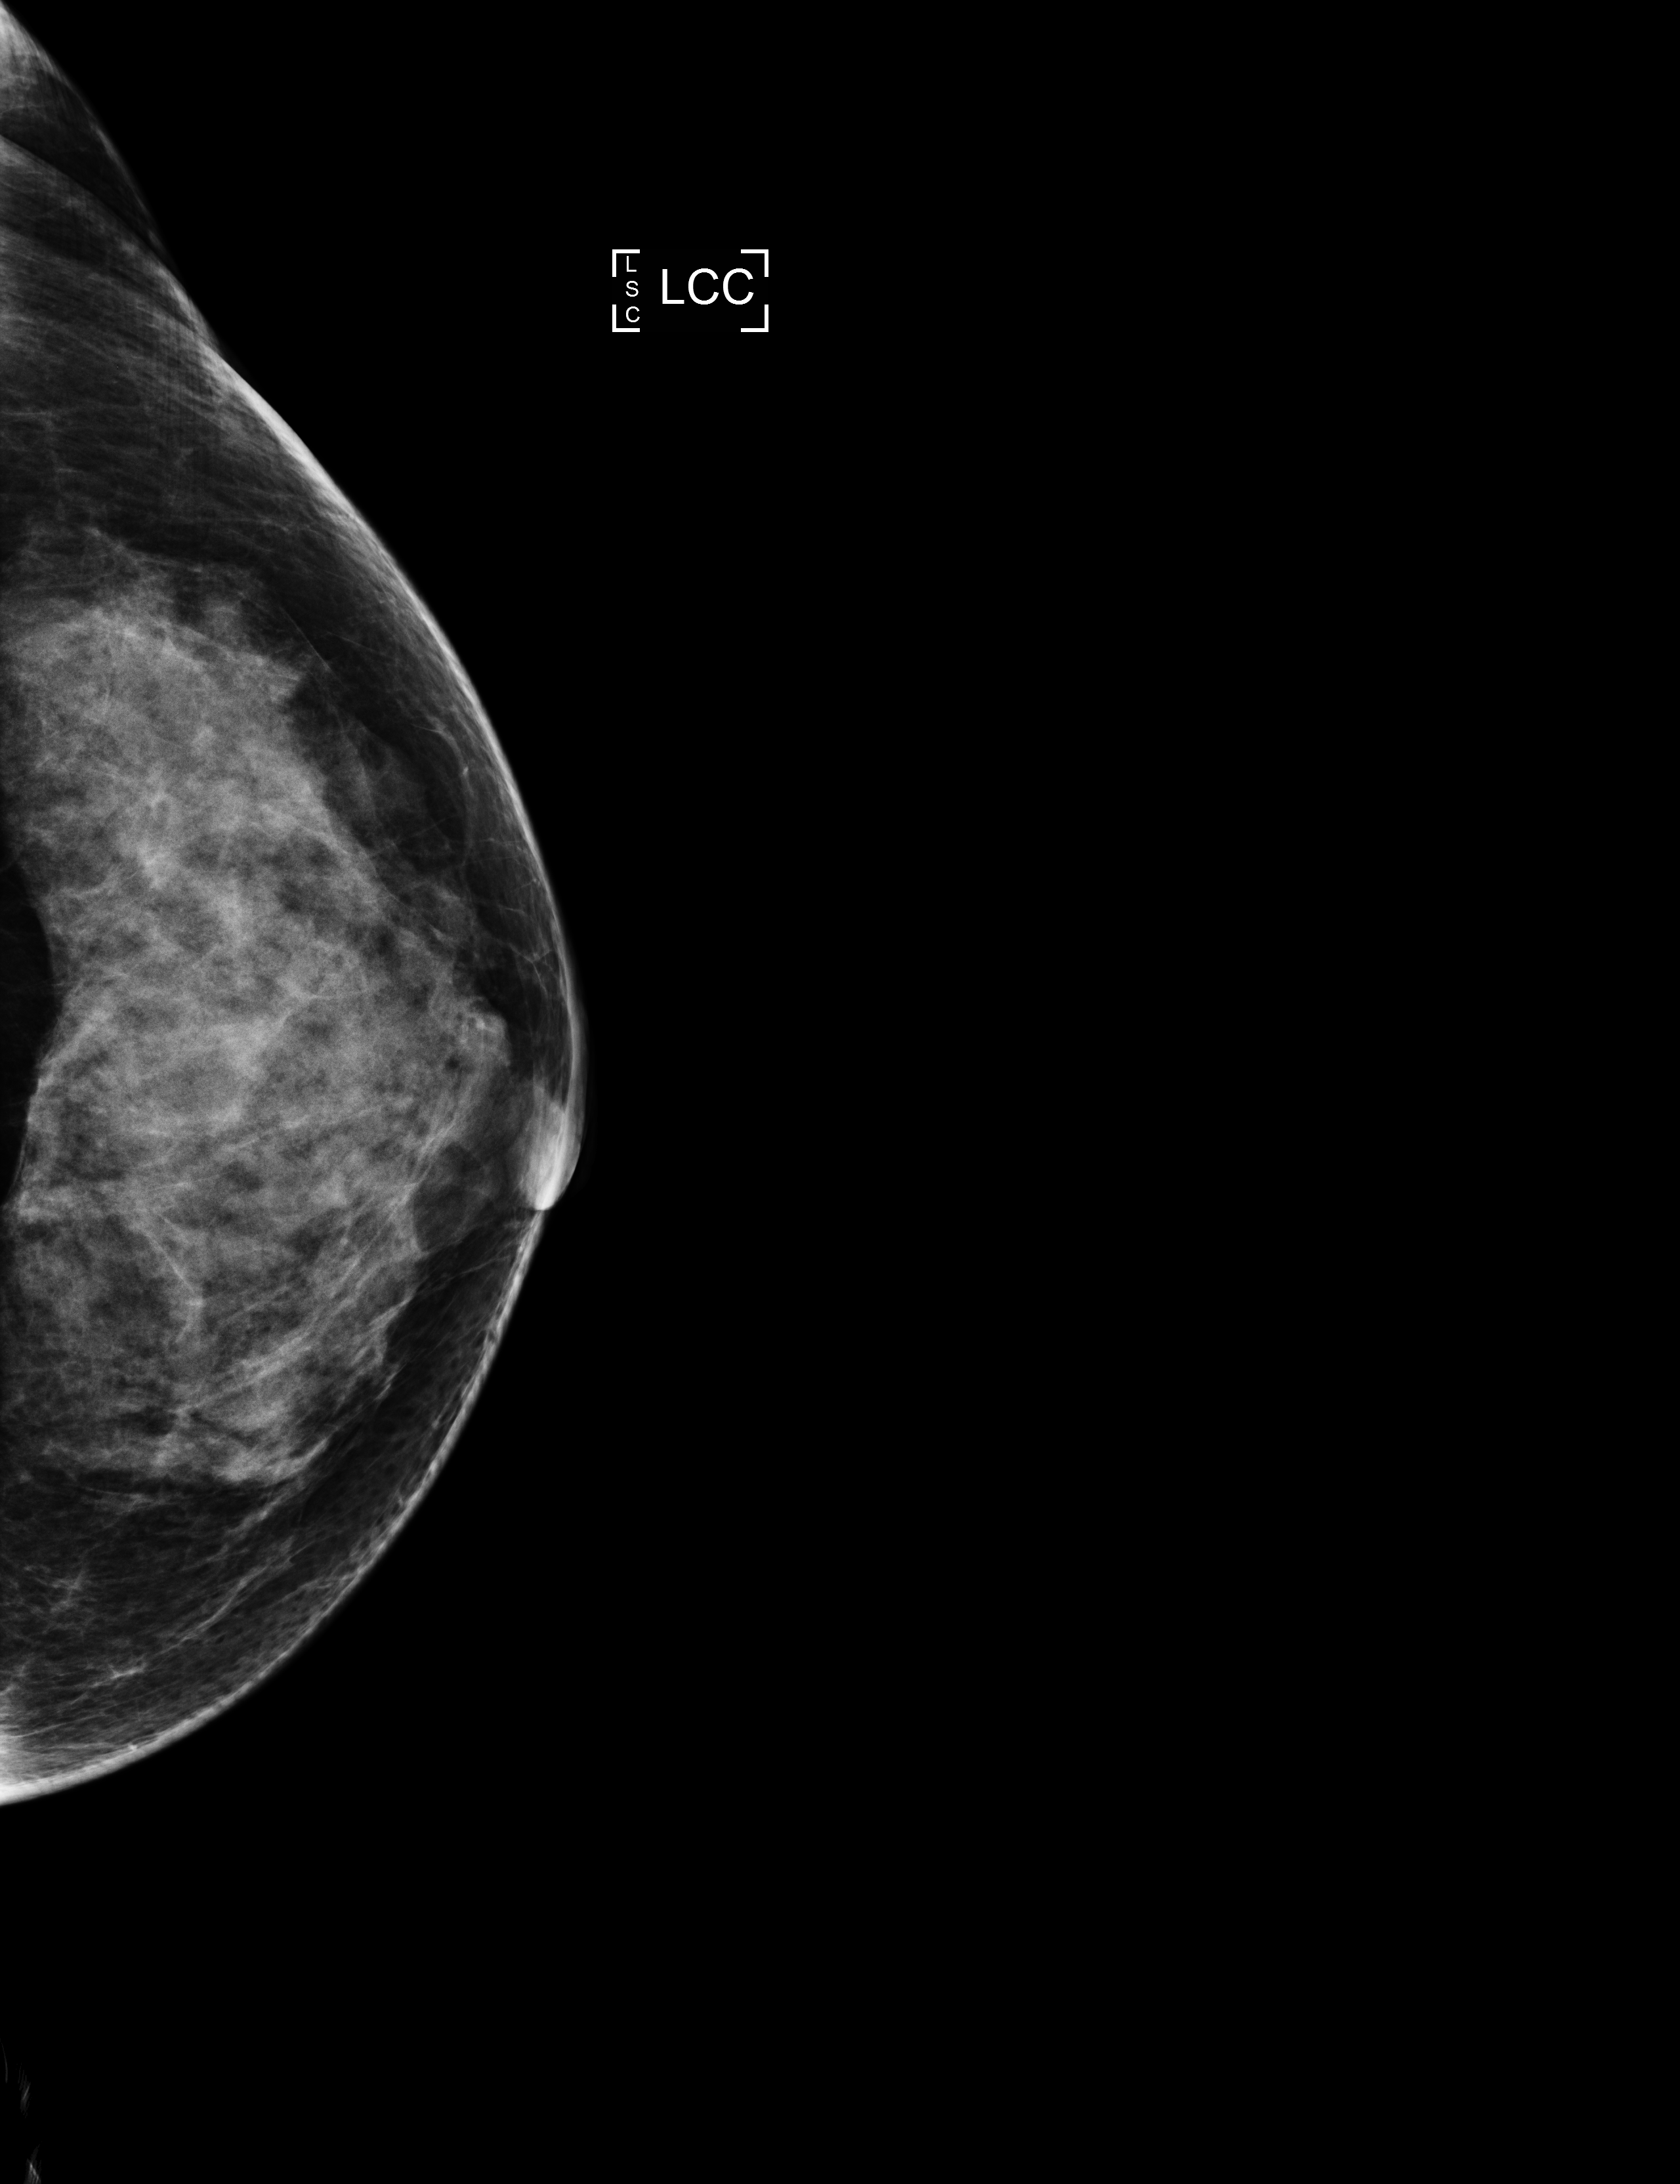
Screening examination. Female patient, age 51 years.
Image type: full-field digital mammogram. Breast: left. Projection: craniocaudal (CC) view.